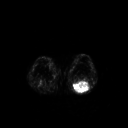
FDG PET of an extremity soft-tissue mass (from a PET/CT study), one axial slice. Position 182 of 267 along the scan axis. 3.27 mm slice thickness. 128 × 128 image matrix, field of view 500 × 500 mm. Male patient, age 54 years. Case-level facts recorded for this patient, not image findings: histological type: synovial sarcoma; site of the primary tumour: left poplietal fossa.
Structures marked on this image (expert contour drawn on MRI and transferred to this co-registered scan by the dataset authors):
- gross tumour volume (mass): bounding box [x1, y1, x2, y2] px = [72, 81, 91, 93]